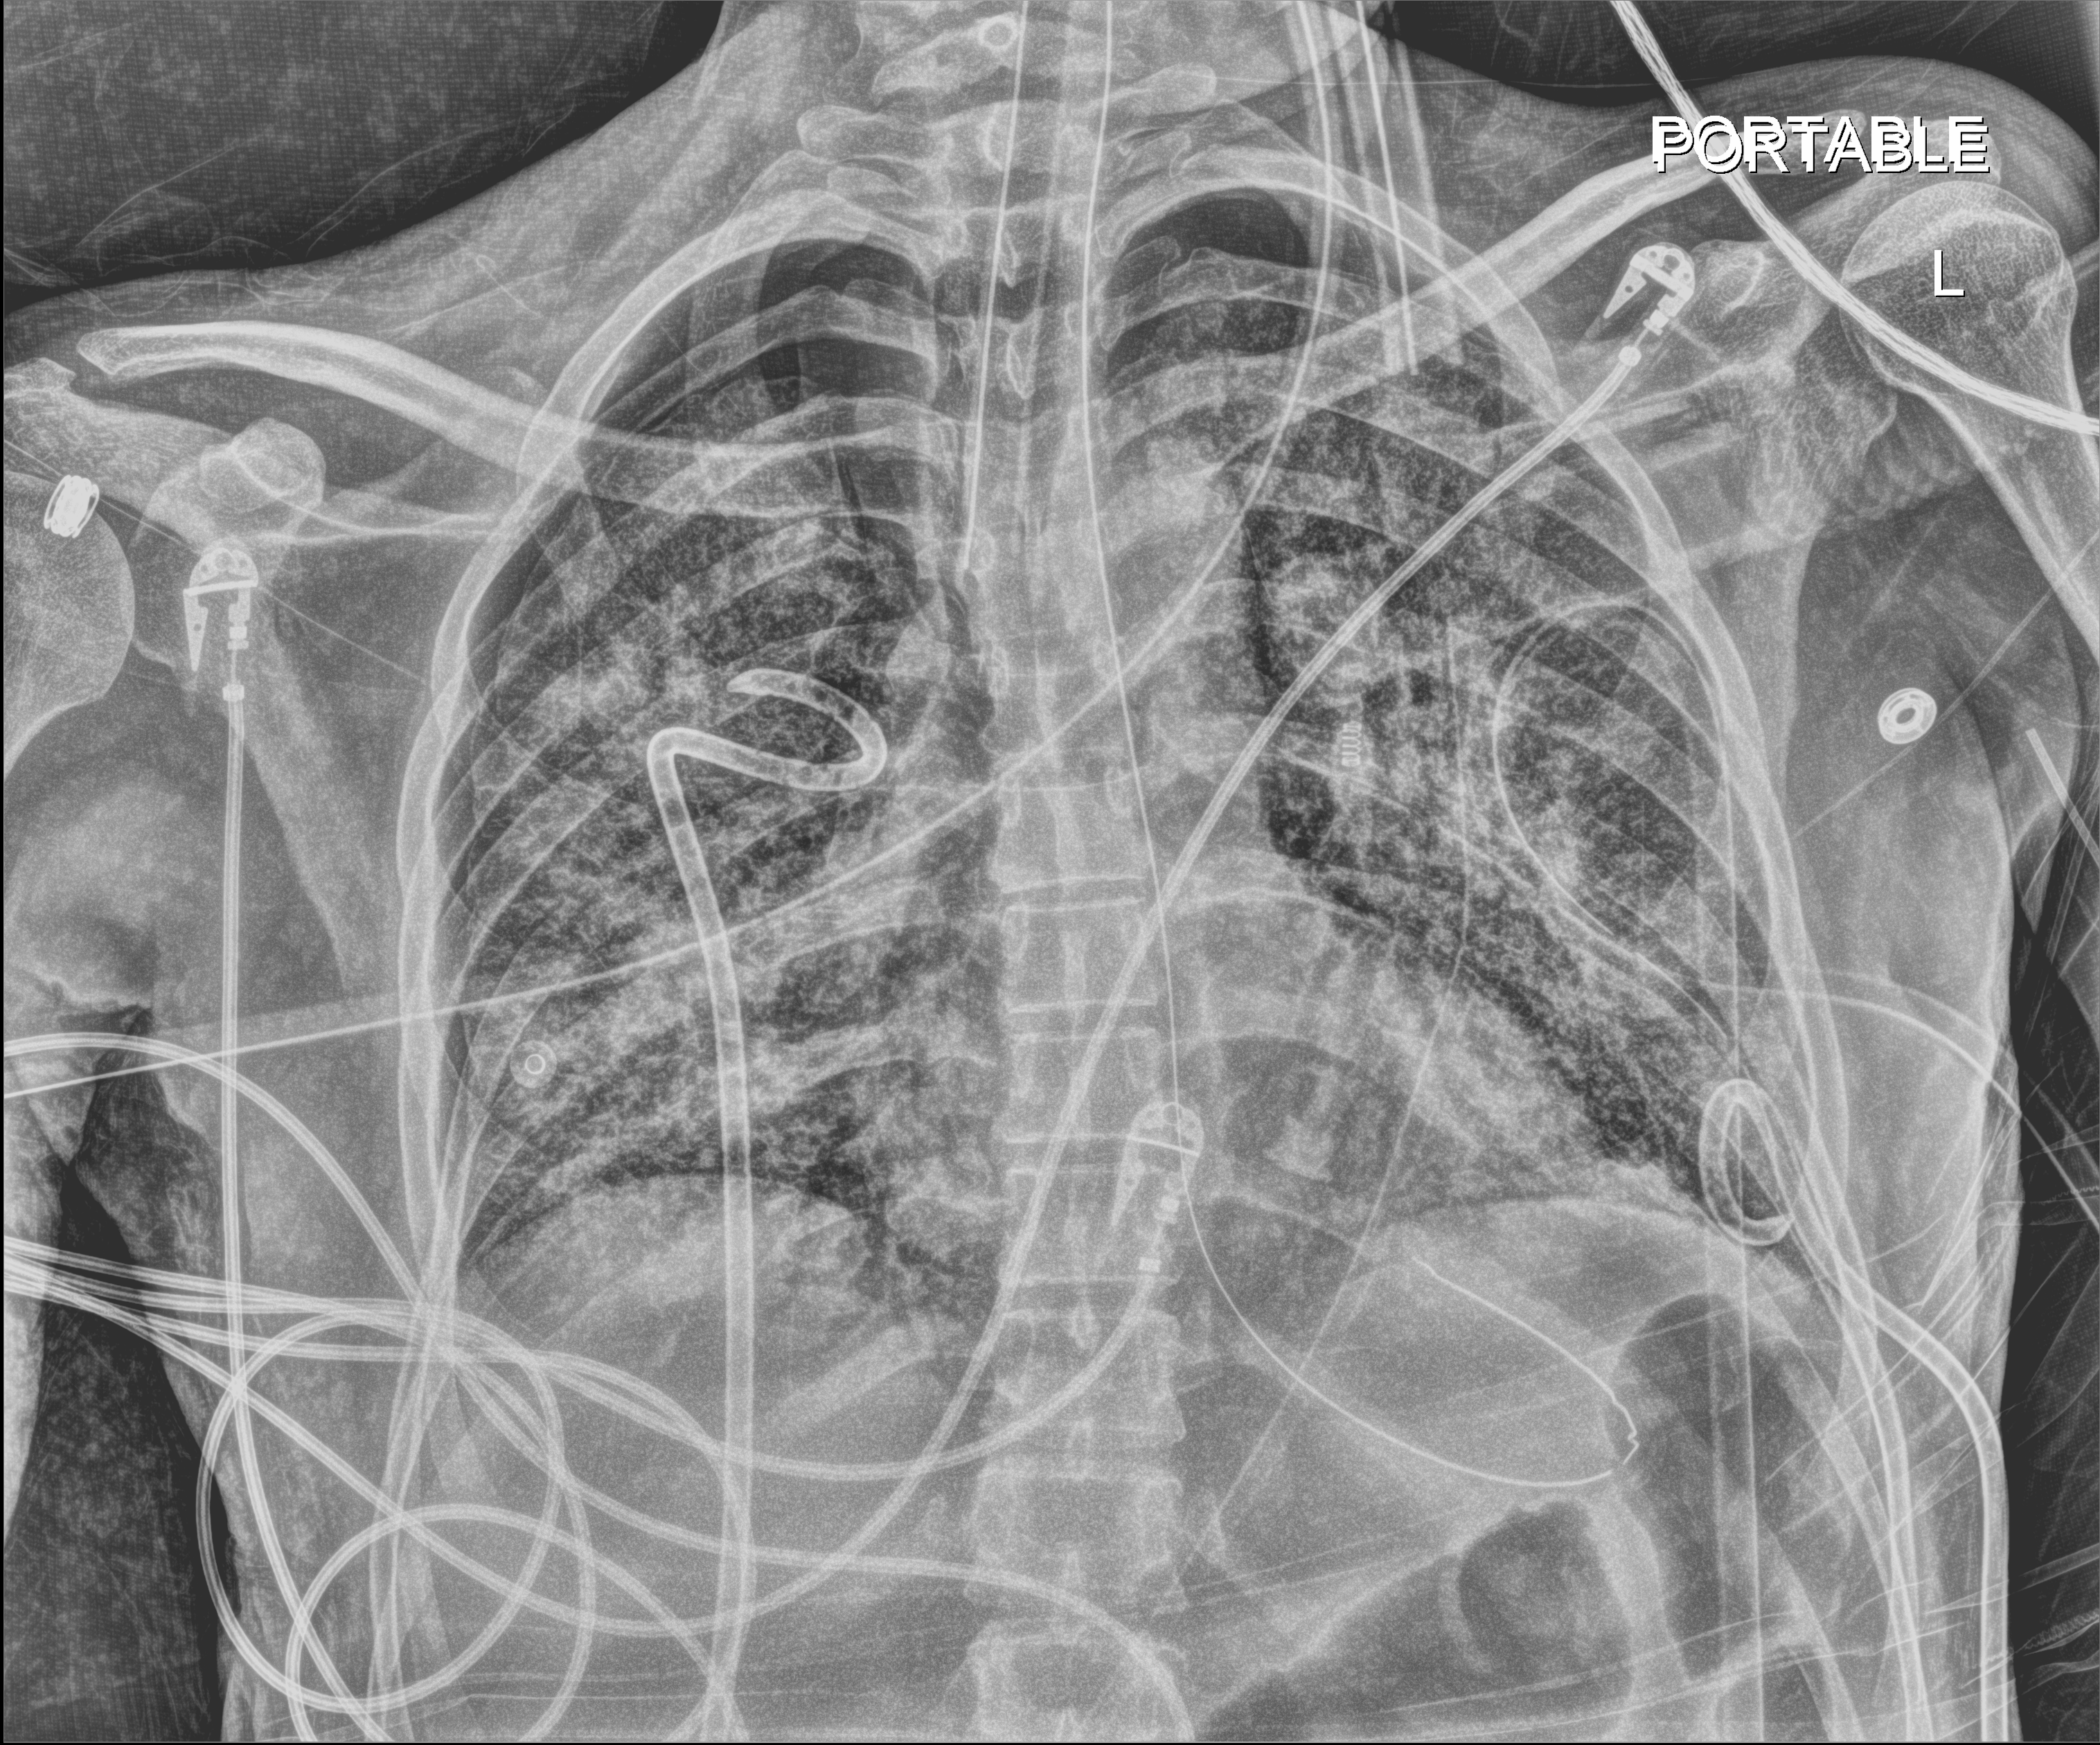
Chest X-ray (portable), anteroposterior (AP) projection. Patient hospitalised with COVID-19, aged 18–59 years.
Admission-level facts for this patient (not findings on this image; timing relative to this image not recorded): admitted to intensive care during this hospital stay: yes; length of hospital stay: 41 days; chronic kidney disease (admission record): no.